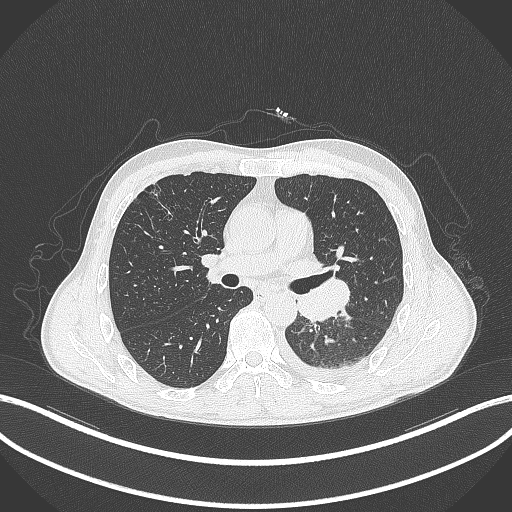
Chest CT, one axial slice; position 184 of 295 along the scan axis; reconstruction kernel B70f; 120 kVp; lung window (W 1500 / L -600 HU); 512 × 512 image matrix, field of view 400 × 400 mm. Patient: male, 47 years. From the clinical record (not read from this slice): clinical TNM (as recorded): T3 N1 M1c.
Annotated regions visible in this slice (rectangle marked by the reading radiologist):
- lung tumour (recorded histology: small cell carcinoma): bounding box (x1, y1, x2, y2) in pixels: (293, 276, 351, 324)